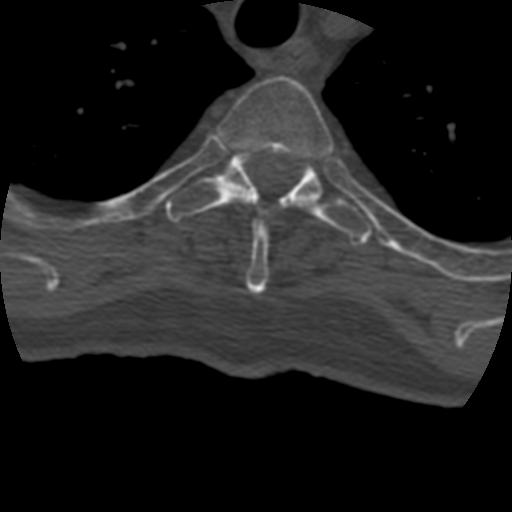
CT including the spine, one axial slice. Slice 344 of 399 in the series (ordered by position). Bone window (W 1800 / L 400 HU). 1.25 mm slice thickness. 512 × 512 image matrix. Patient age 69 years. Case-level facts recorded for this patient, not image findings: primary cancer: prostate.
Structures marked on this image (semi-automatic segmentation, software-assisted and operator-edited):
- T3 vertebra: bounding box (x1, y1, x2, y2) in pixels: (219, 76, 334, 295)
- T4 vertebra: (166, 151, 373, 246)